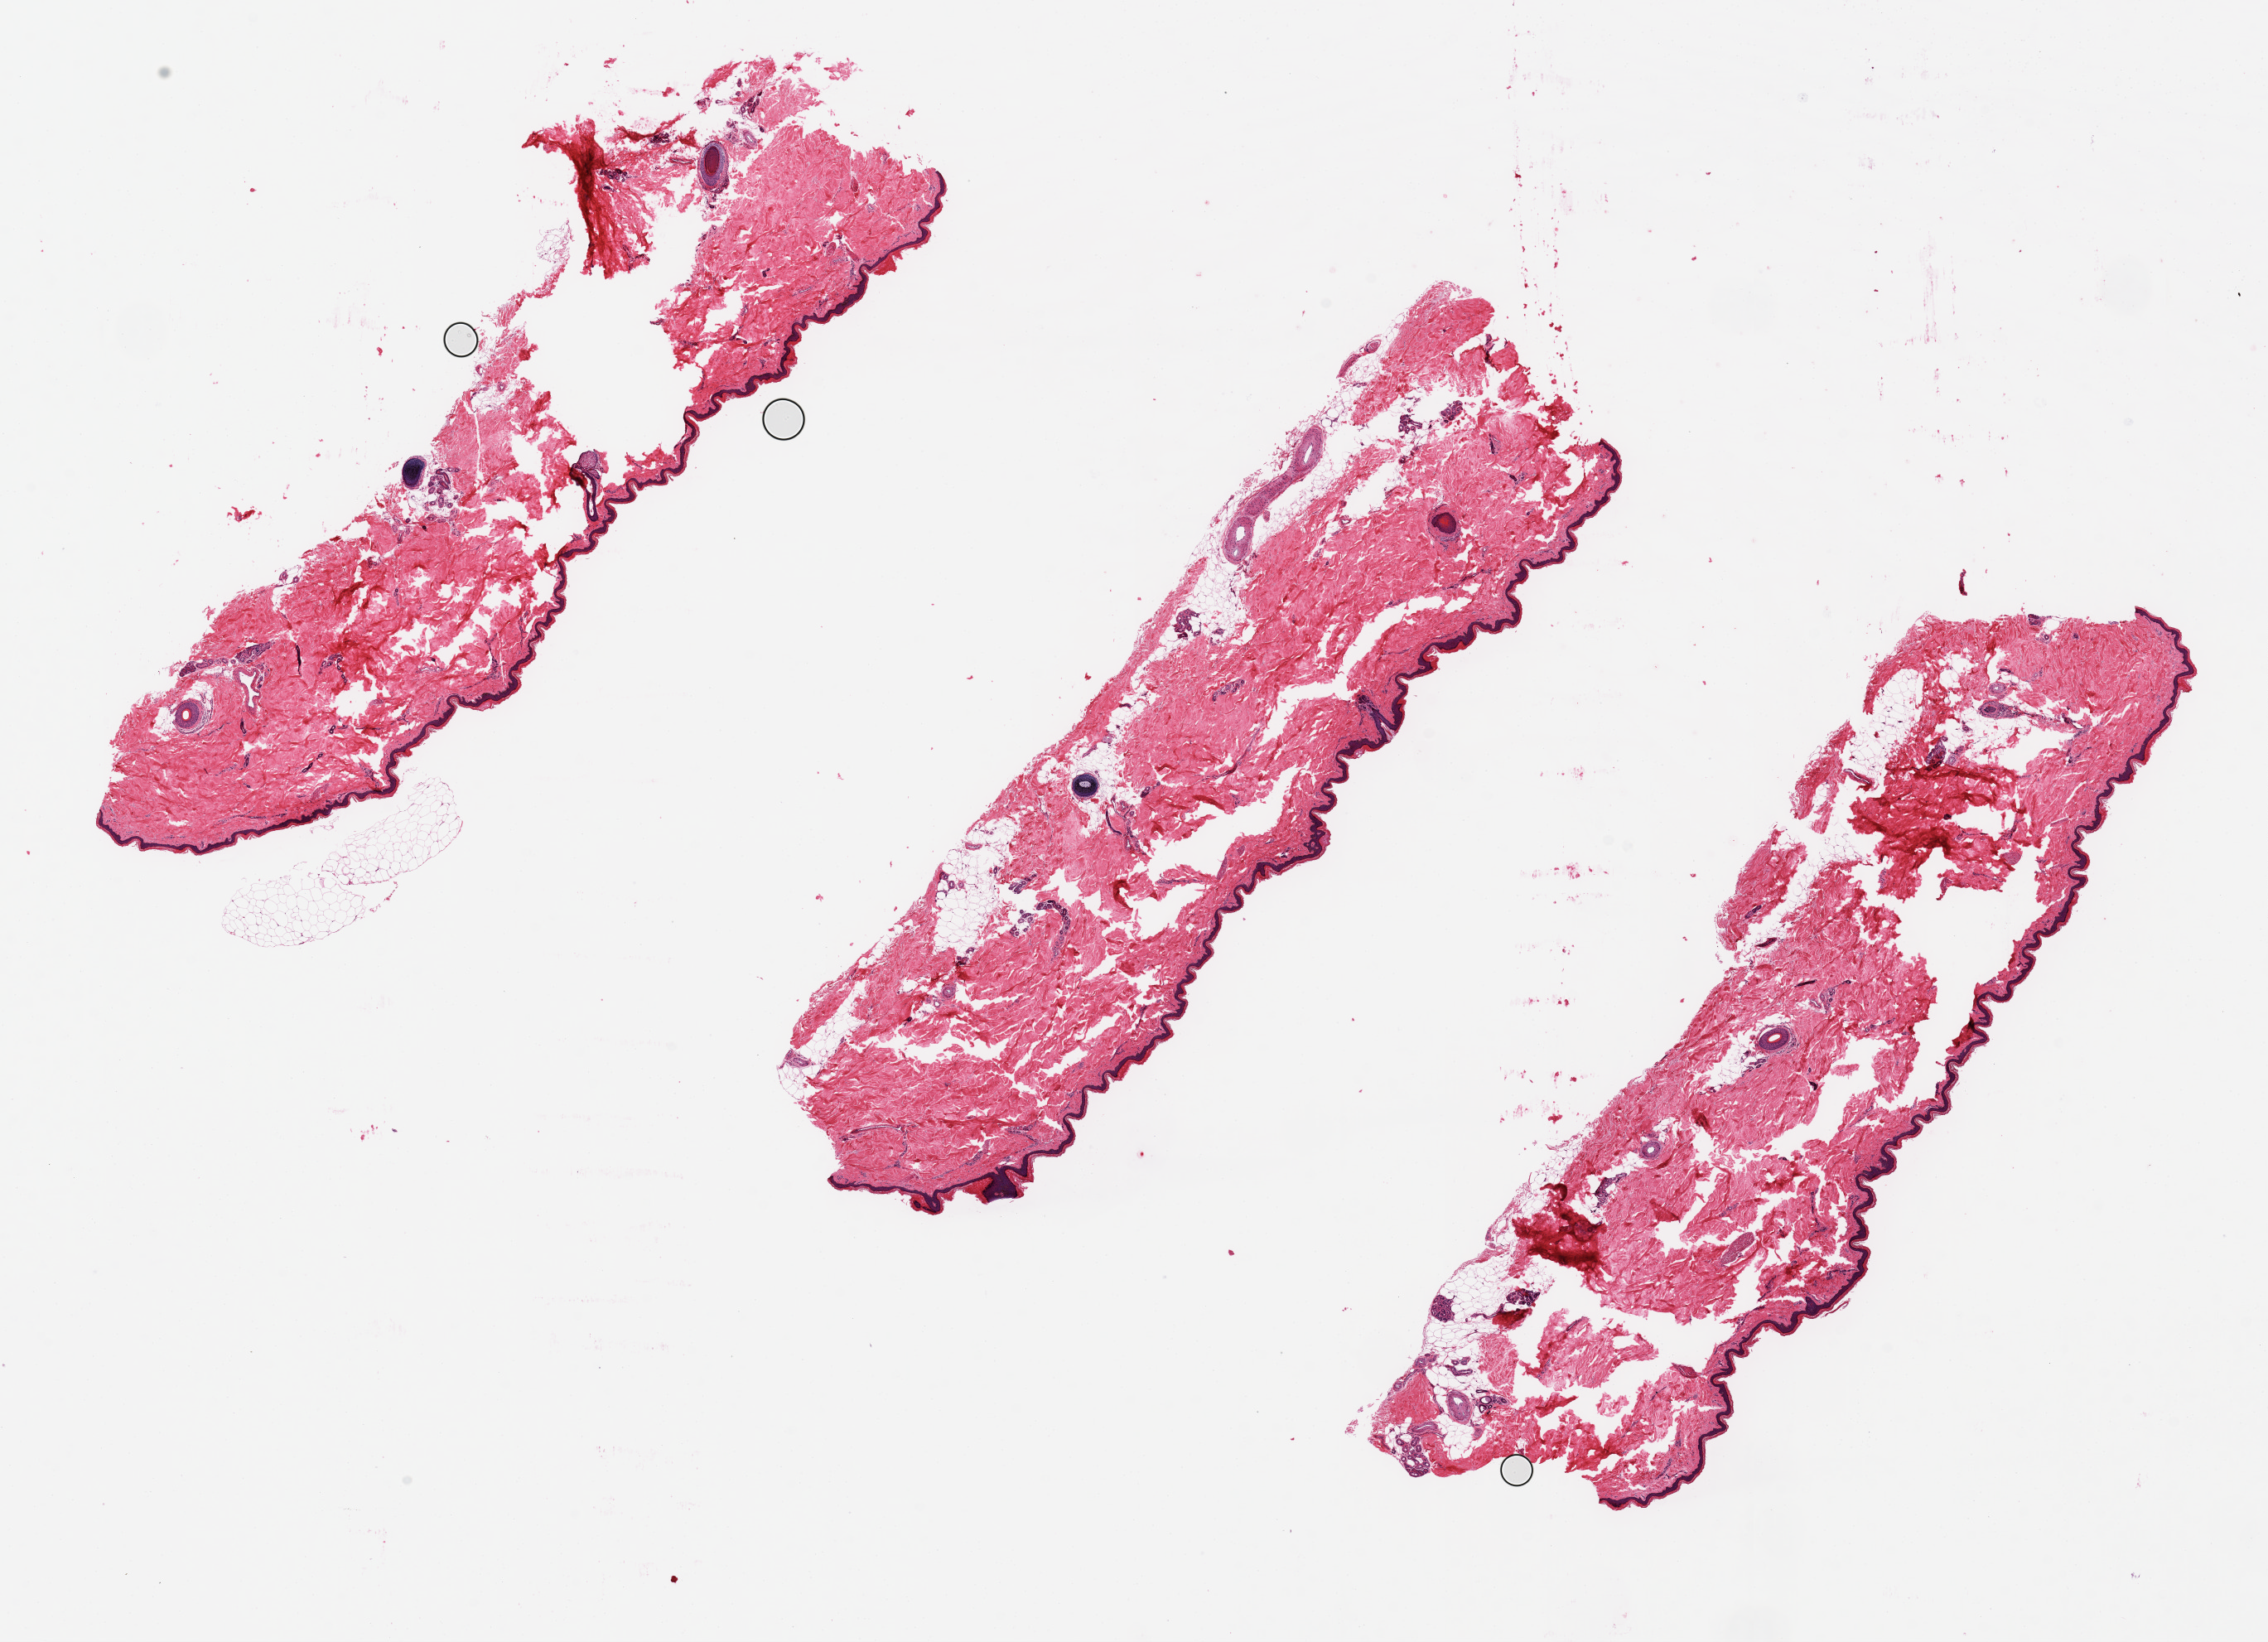
Digitized haematoxylin and eosin-stained section, low-resolution overview of the scanned area, about 21.7 x 15.7 mm; PAXgene-fixed, paraffin-embedded tissue; sampled site (target tissue): skin of lower leg; tissue donor sample. Donor sex: male.
Reviewer comment on this tissue sample: OK for anlysis.